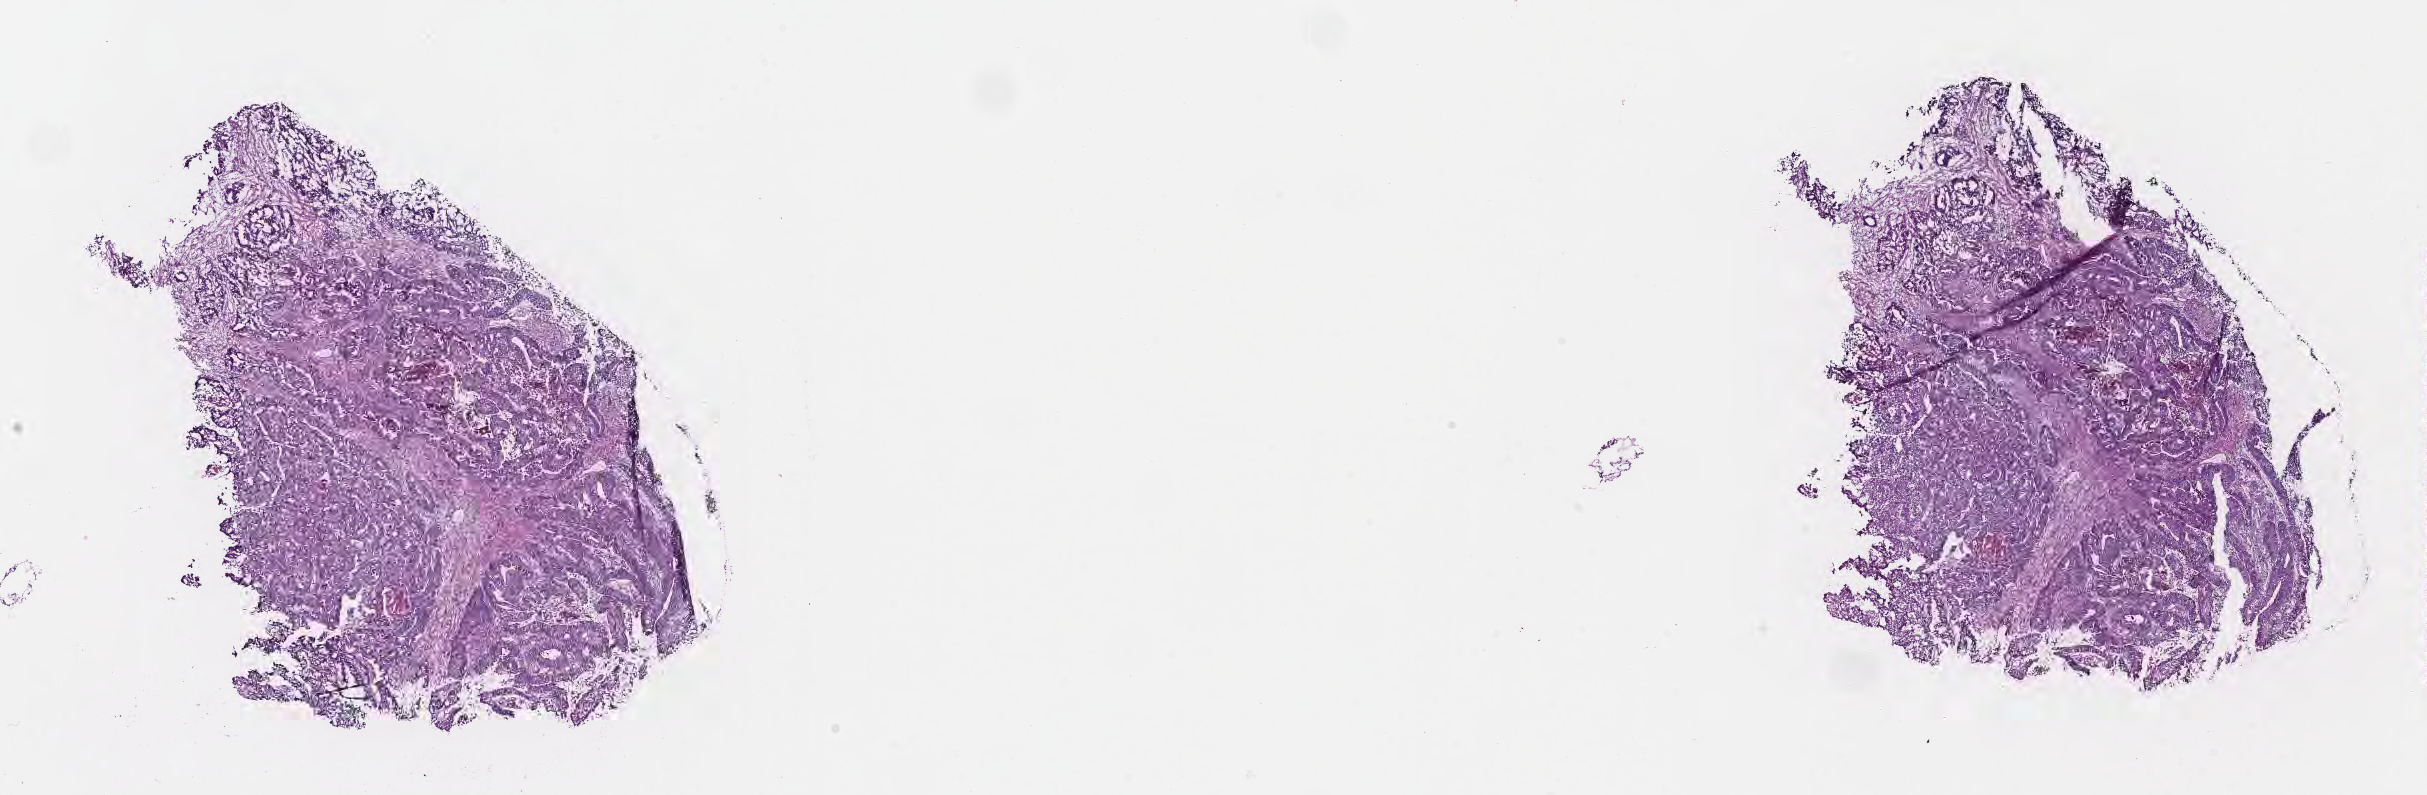
Digitized hematoxylin and eosin (H&E)-stained section, shown as a low-resolution overview of the whole scanned area (about 19.6 x 6.4 mm). Frozen section. Primary tumor. Female patient; age at initial diagnosis 76 years. Tumor grade: G2 (moderately differentiated). Pathologist review of this section (percent, as recorded): tumor cells 85%, tumor nuclei 85%, stromal cells 14%, necrosis 1%, normal cells 0%. Infiltration values recorded for this section: lymphocyte infiltration 3%, monocyte infiltration 1%, neutrophil infiltration 5%.
* diagnosis: Adenocarcinoma, metastatic, NOS
* AJCC pathologic stage: Stage IVA